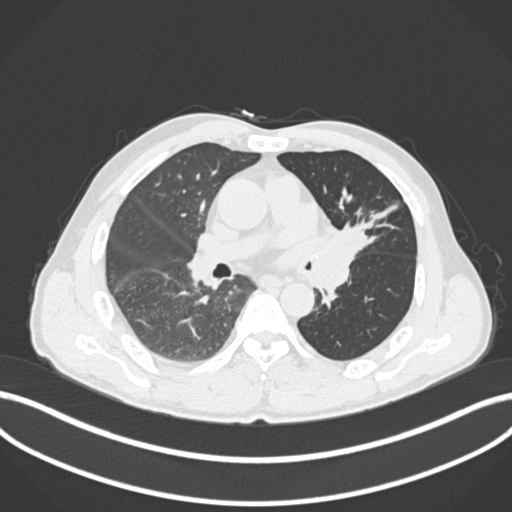
Chest CT, one axial slice. Reconstruction kernel B30f. 120 kVp. Lung window (W 1500 / L -600 HU). 512 × 512 image matrix. Male patient, age 57 years. Case-level facts recorded for this patient, not image findings: clinical TNM (as recorded): T2b N0 M0.
Outlined on this slice (rectangle marked by the reading radiologist):
- lung tumour (recorded histology: squamous cell carcinoma): box from (x=323, y=221) to (x=372, y=268) px